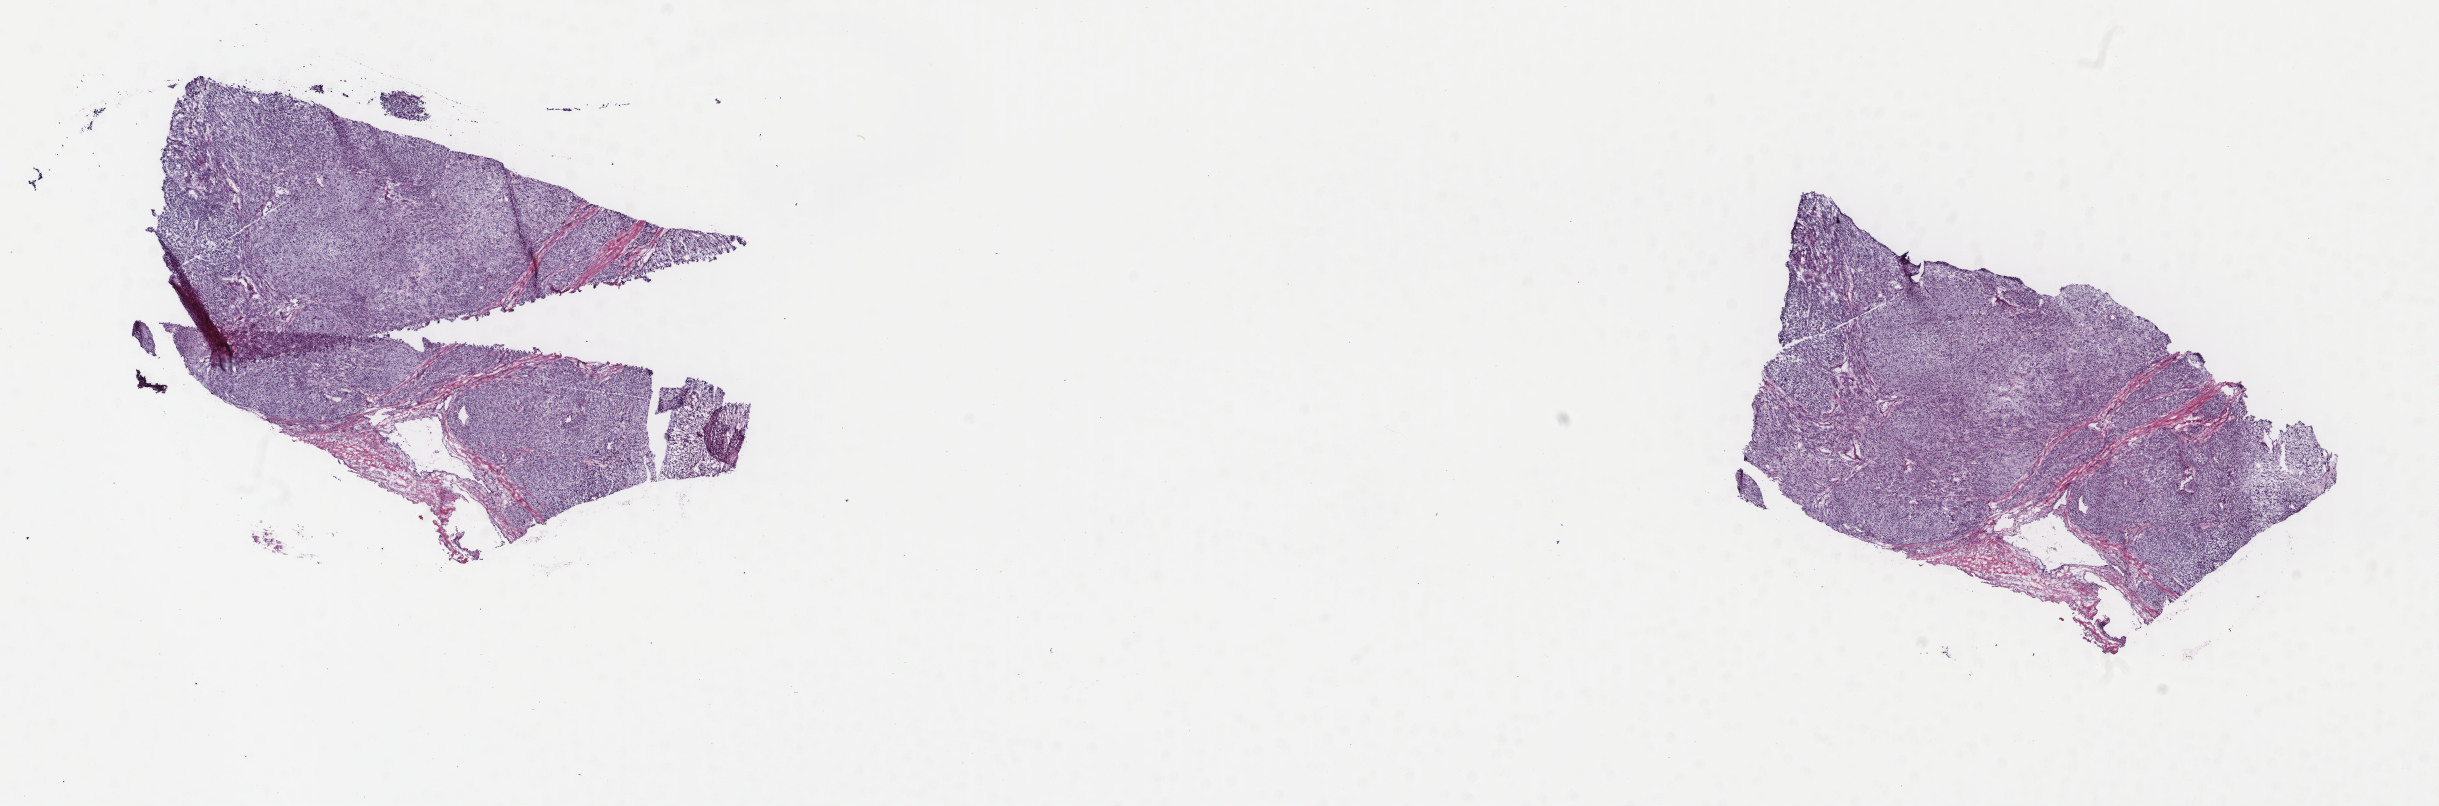
Digitized H&E tissue section (whole slide) — a low-resolution overview of the entire scanned area, about 19.4 x 6.4 mm (from a 40x scan). Frozen section from the top of the tissue portion. Metastatic tumour sample, sampled site not recorded. Male, age 35 years at initial diagnosis. Pathologist review of this section (percent, as recorded): tumour cells 95%, tumour nuclei 98%, normal cells 0%, stromal cells 5%, necrosis 0%. Inflammatory infiltration, as recorded: lymphocyte infiltration 0%, monocyte infiltration 0%, neutrophil infiltration 0%.
This section: metastatic tumour tissue. Patient diagnosis: Malignant melanoma, NOS.